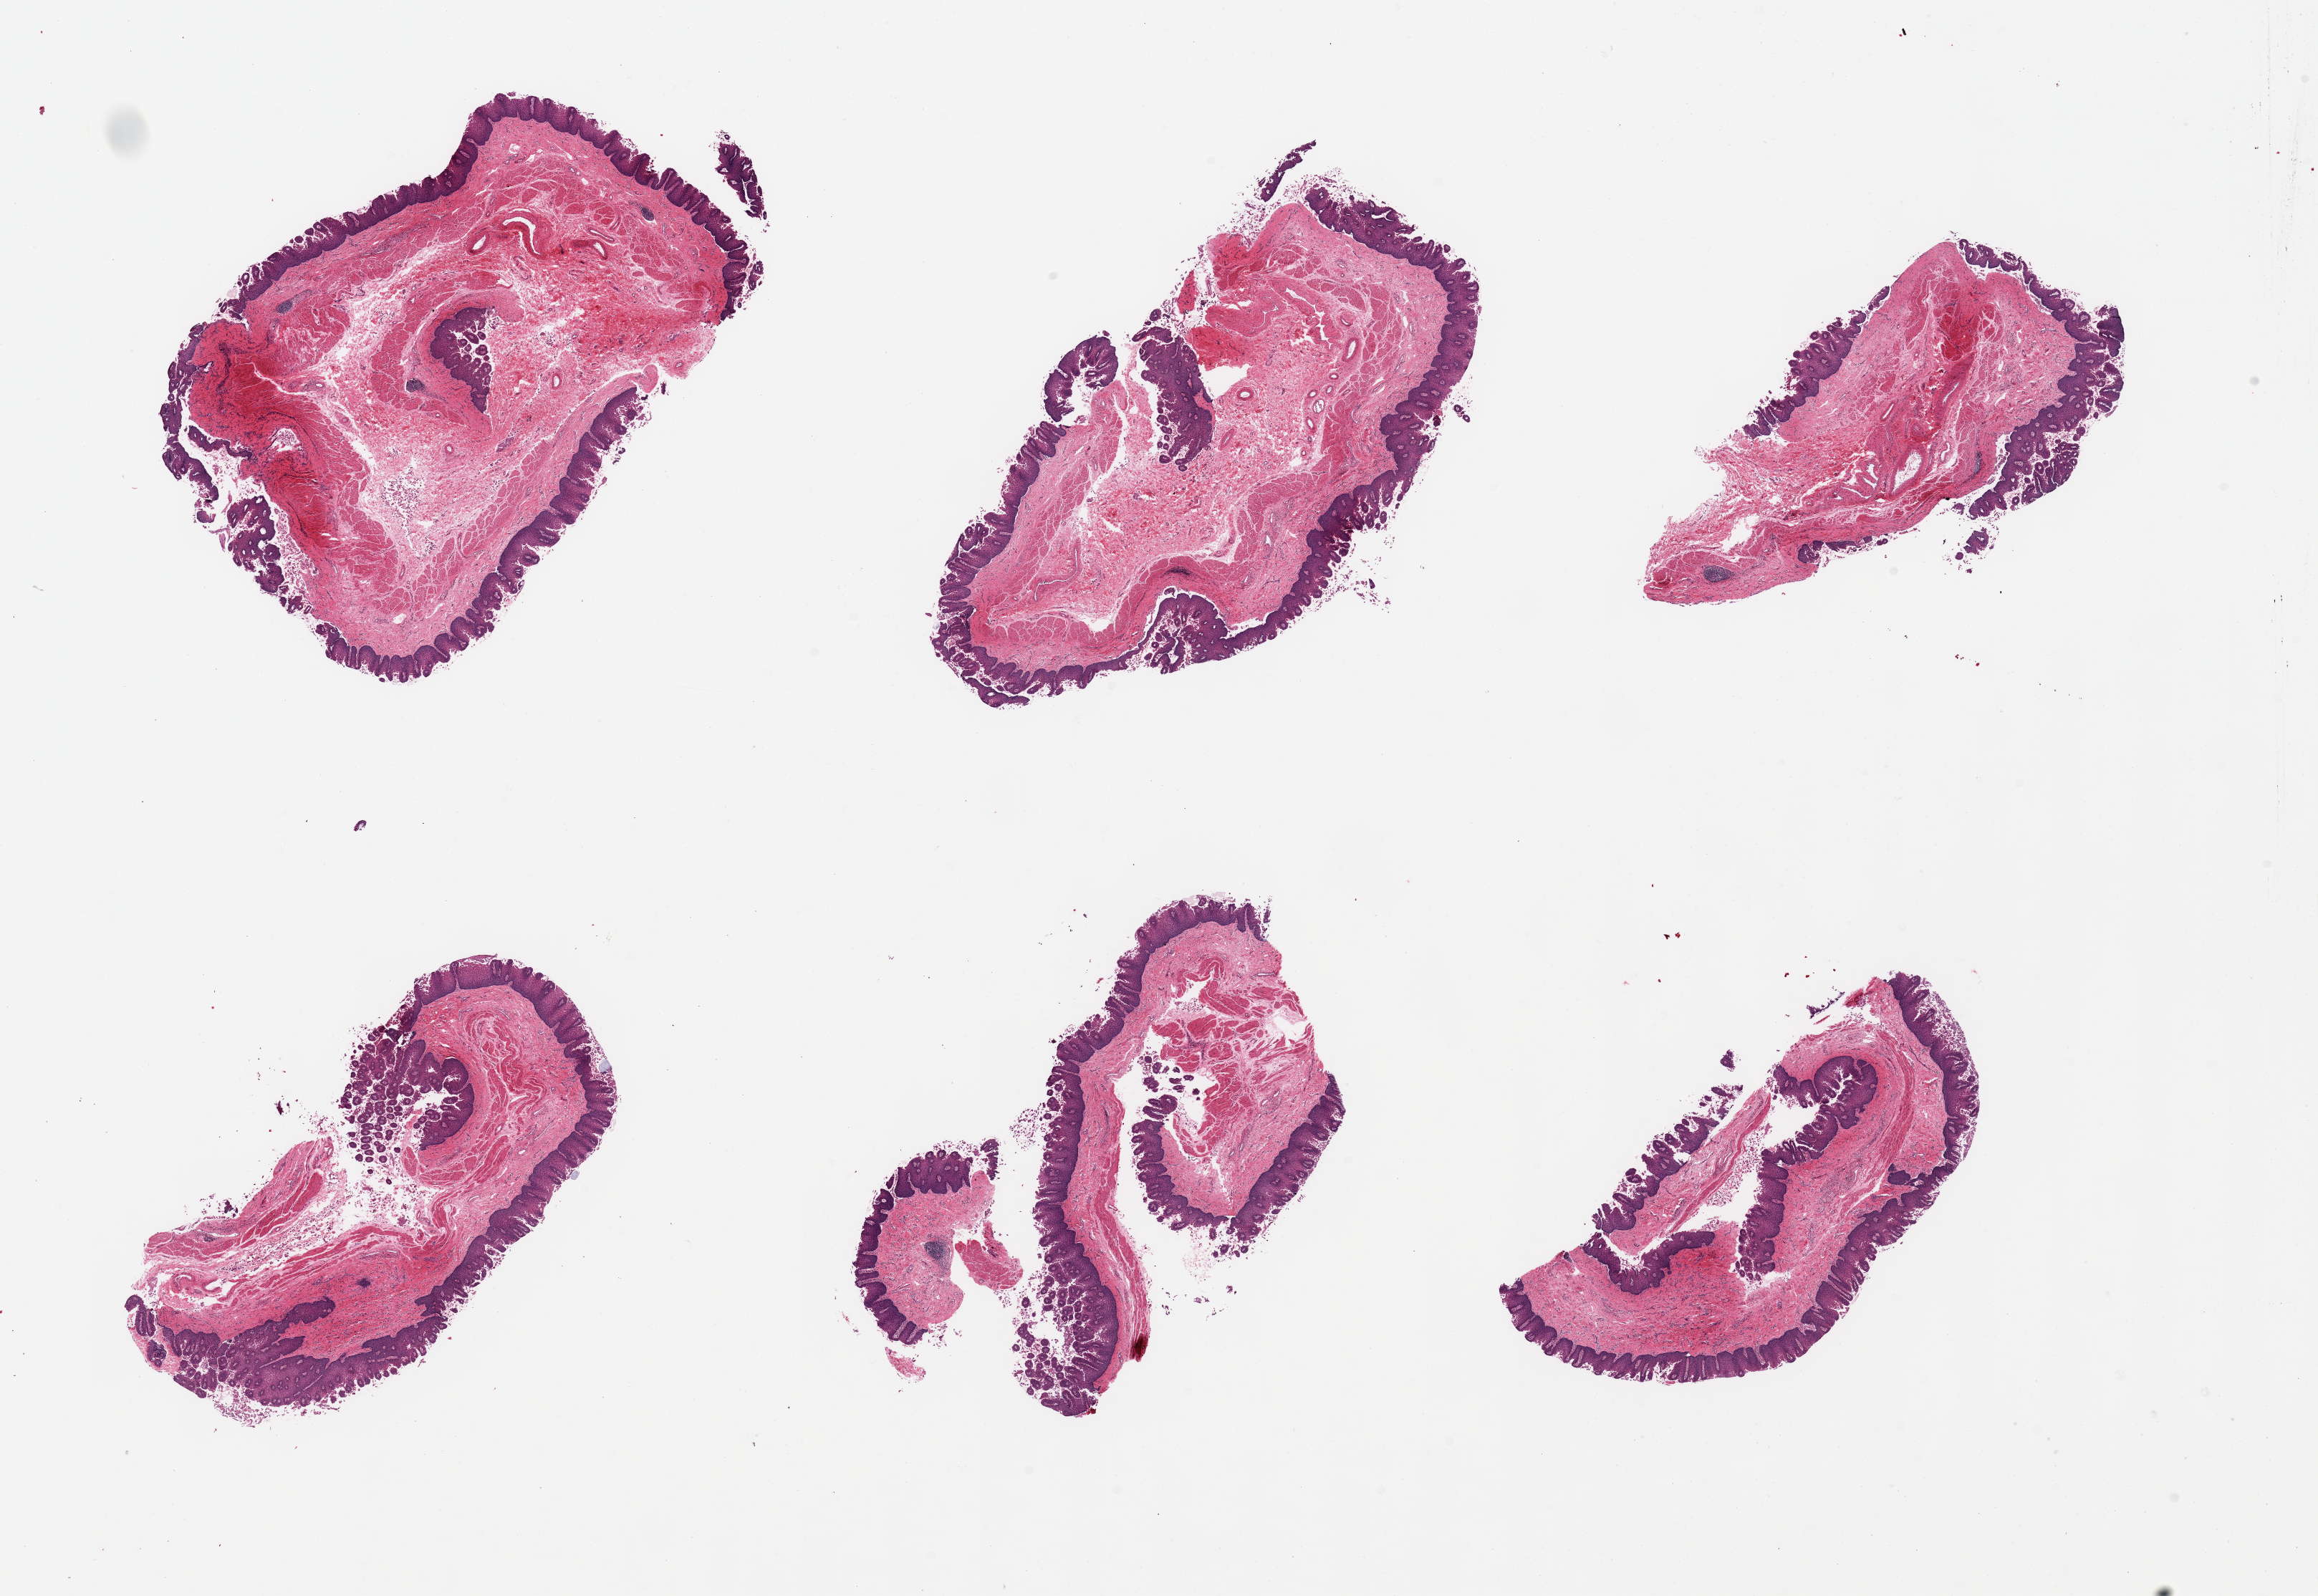
Haematoxylin and eosin whole-slide image — whole scanned area (about 25.6 x 17.6 mm, from a 20x scan) shown as a low-resolution overview, PAXgene-fixed paraffin-embedded (PFPE) section, target tissue: esophageal muscle, tissue donor sample. Male donor.
Pathologist's review note for this sample: 6 pieces; mucosa, not muscularis, squamous hyperplasia and intraepithelial eosinophils and lymphocytes consistent with reflux.